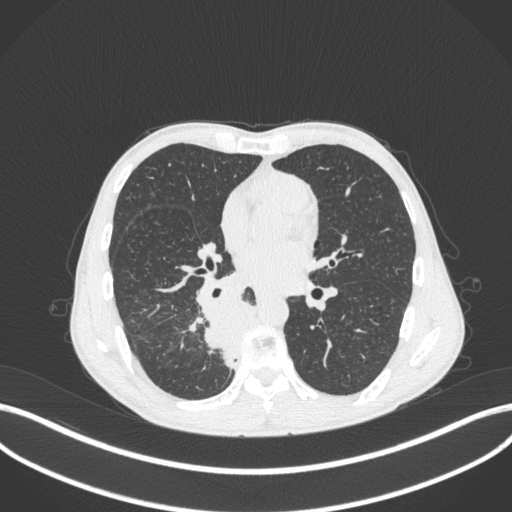
Chest CT, one axial slice. Slice 185 of 371 in the series (ordered by position). Reconstruction kernel B31f. Lung window (W 1500 / L -600 HU). 1 mm slice thickness. 512 × 512 image matrix, field of view 400 × 400 mm. Male patient, age 58 years. Case-level facts recorded for this patient, not image findings: clinical TNM (as recorded): T3 N1 M1.
Outlined on this slice (bounding box drawn by a radiologist):
- lung tumour (recorded histology: squamous cell carcinoma): bounding box (x1, y1, x2, y2) in pixels: (194, 294, 255, 369)